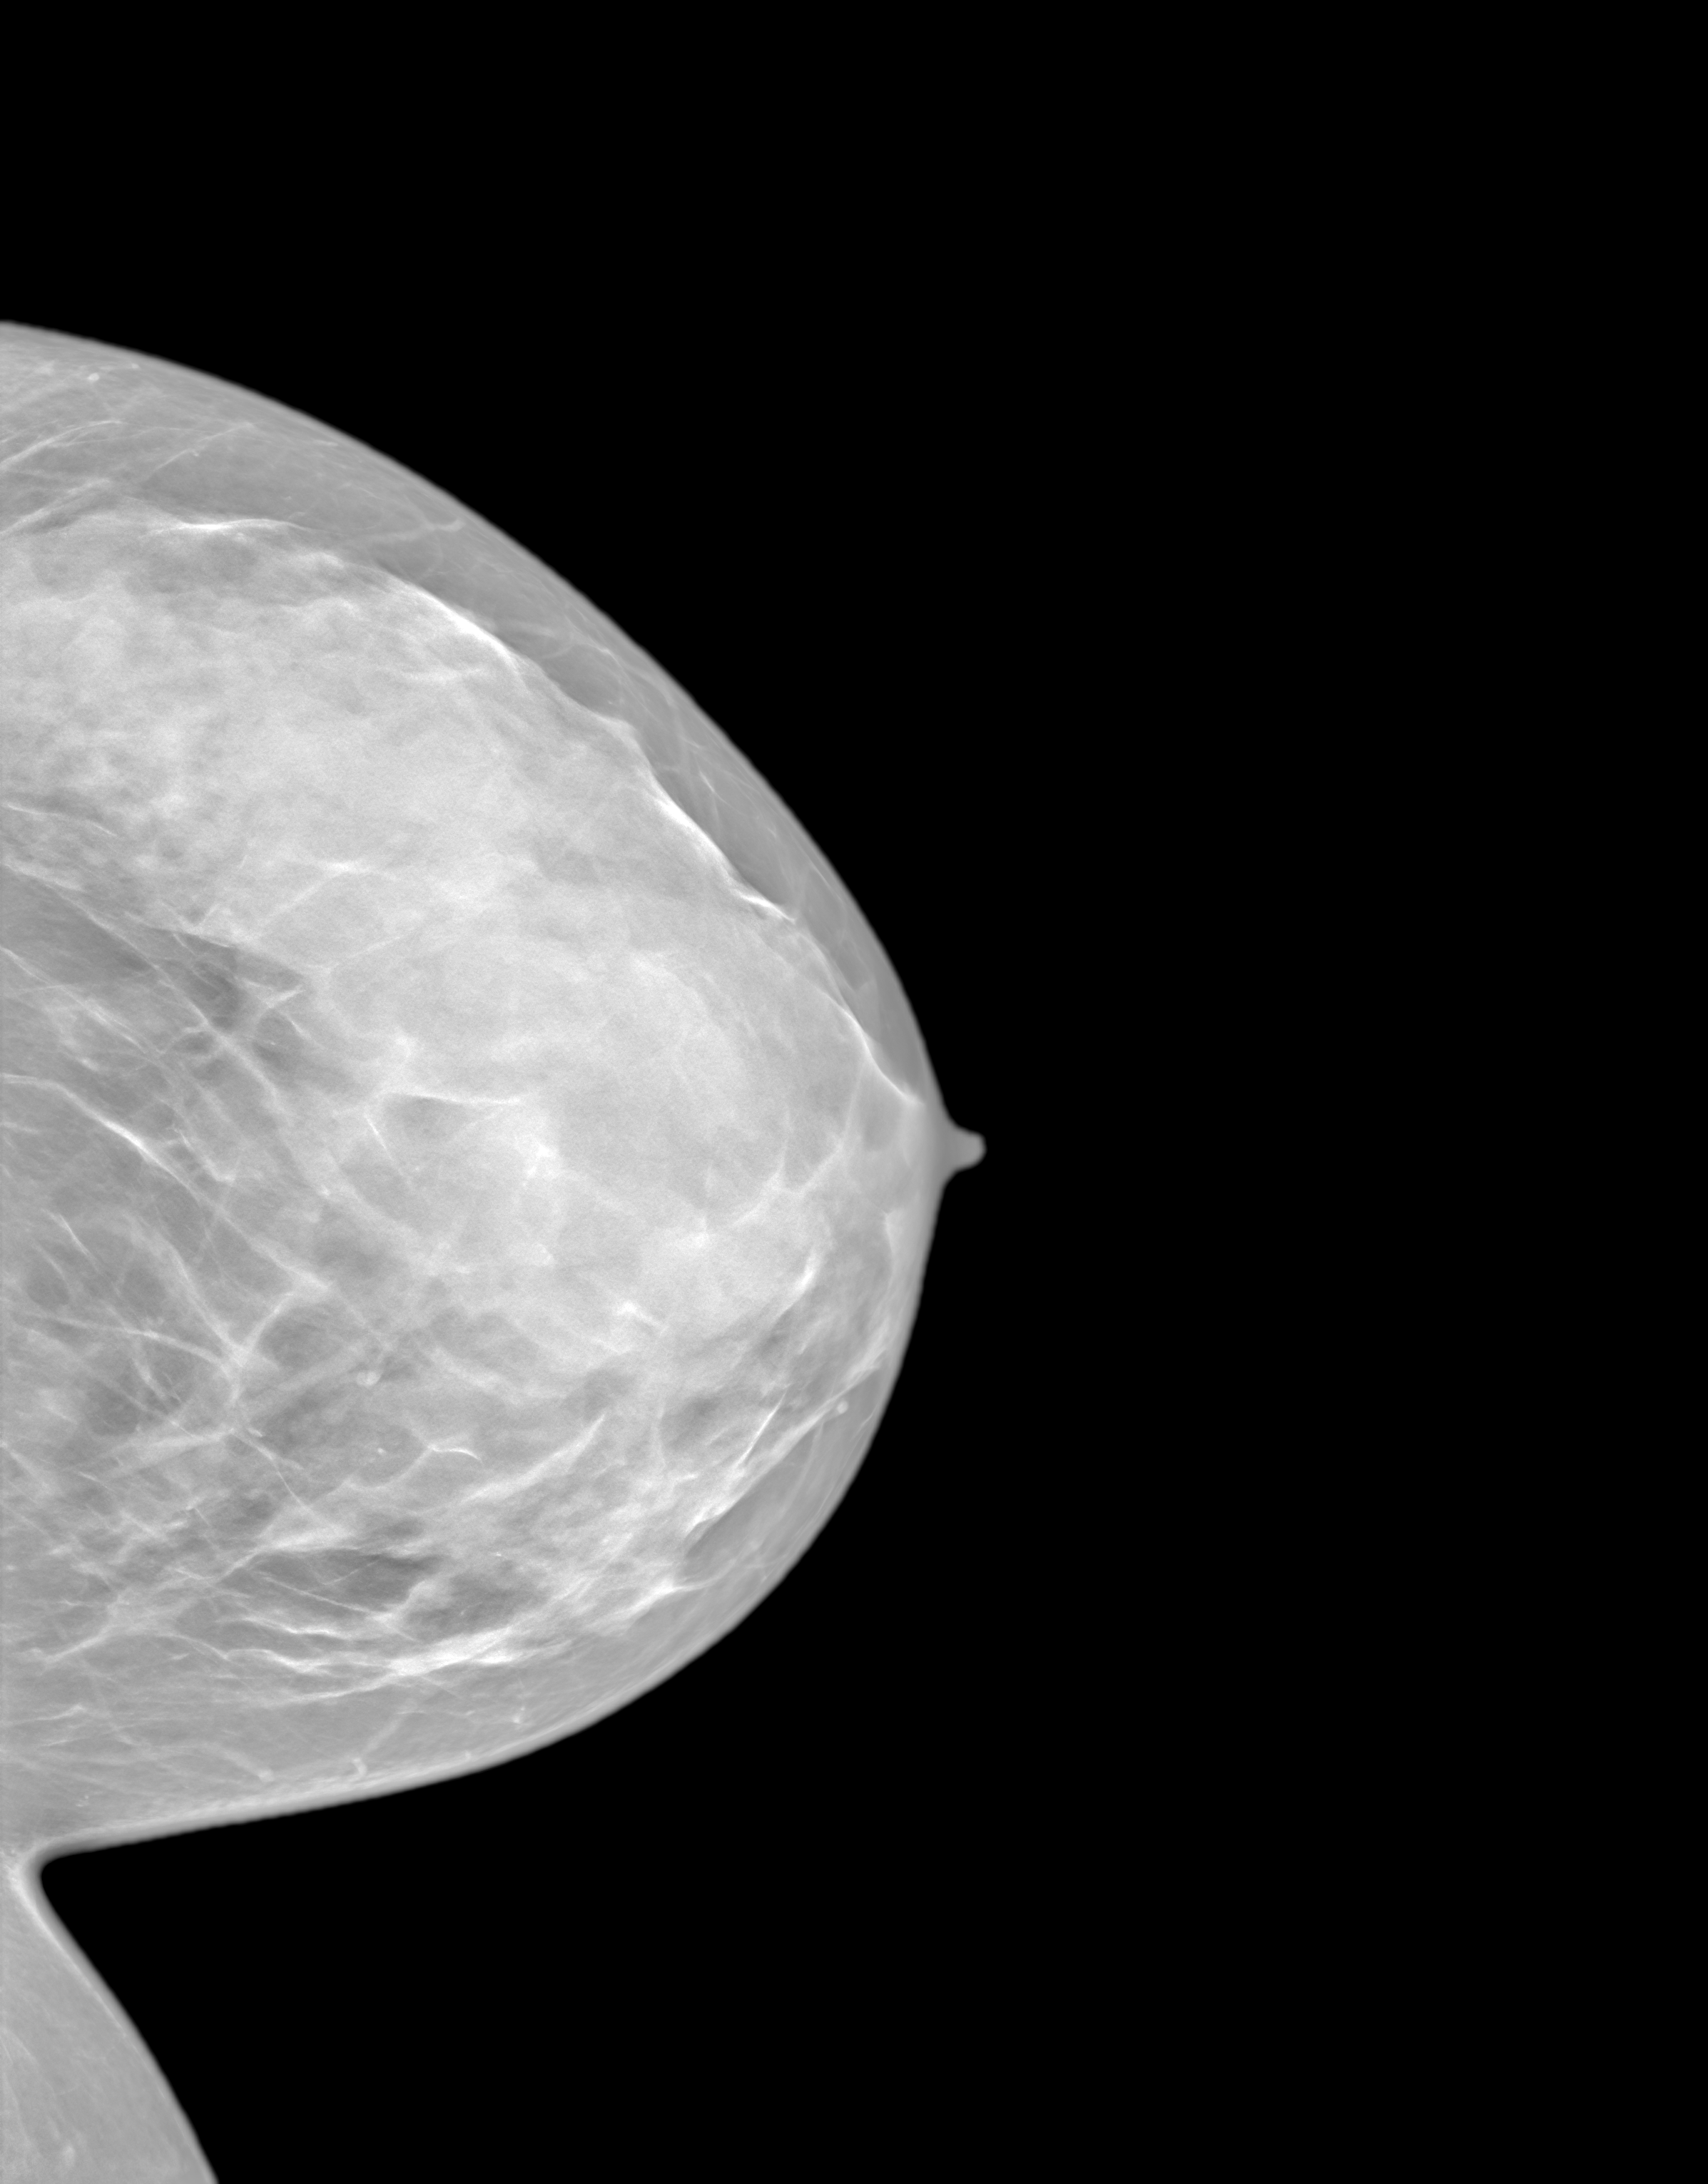
Synthesized 2-D mammogram reconstructed from digital breast tomosynthesis, left breast, craniocaudal (CC) view, screening examination. Patient: female, 43 years.
BI-RADS breast density category at the screening exam (both breasts, scale 1–4): 4. Final BI-RADS assessment for this screening round (tomosynthesis exam, both breasts): category 1. Recall: no recall after this screen.